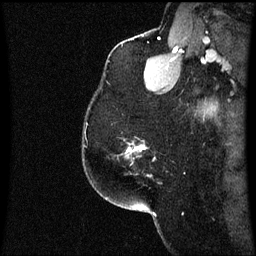
Breast MRI (dynamic contrast-enhanced), one sagittal slice. Position 49 of 60 along the scan axis. Dynamic contrast-enhanced series, image 2 of 3 at this slice position (ordered by acquisition). 1.5 T. TE 4.2 ms, TR 8.9 ms. 2 mm slice thickness. 256 × 256 image matrix, field of view 200 × 200 mm. Female patient, age 58 years. From the clinical record (not read from this slice): setting: breast cancer imaged before/during neoadjuvant chemotherapy; receptor status: triple-negative.
Annotated regions visible in this slice (semi-automatic segmentation, software-assisted and operator-edited):
- analysis volume of interest (the breast-tissue region the enhancement analysis was run in; not a lesion): bounding box <126,140,155,177> (left, top, right, bottom; pixels)
- tumour enhancement mask (voxels above the 70 % enhancement threshold inside the analysis volume of interest): <126,146,145,157>